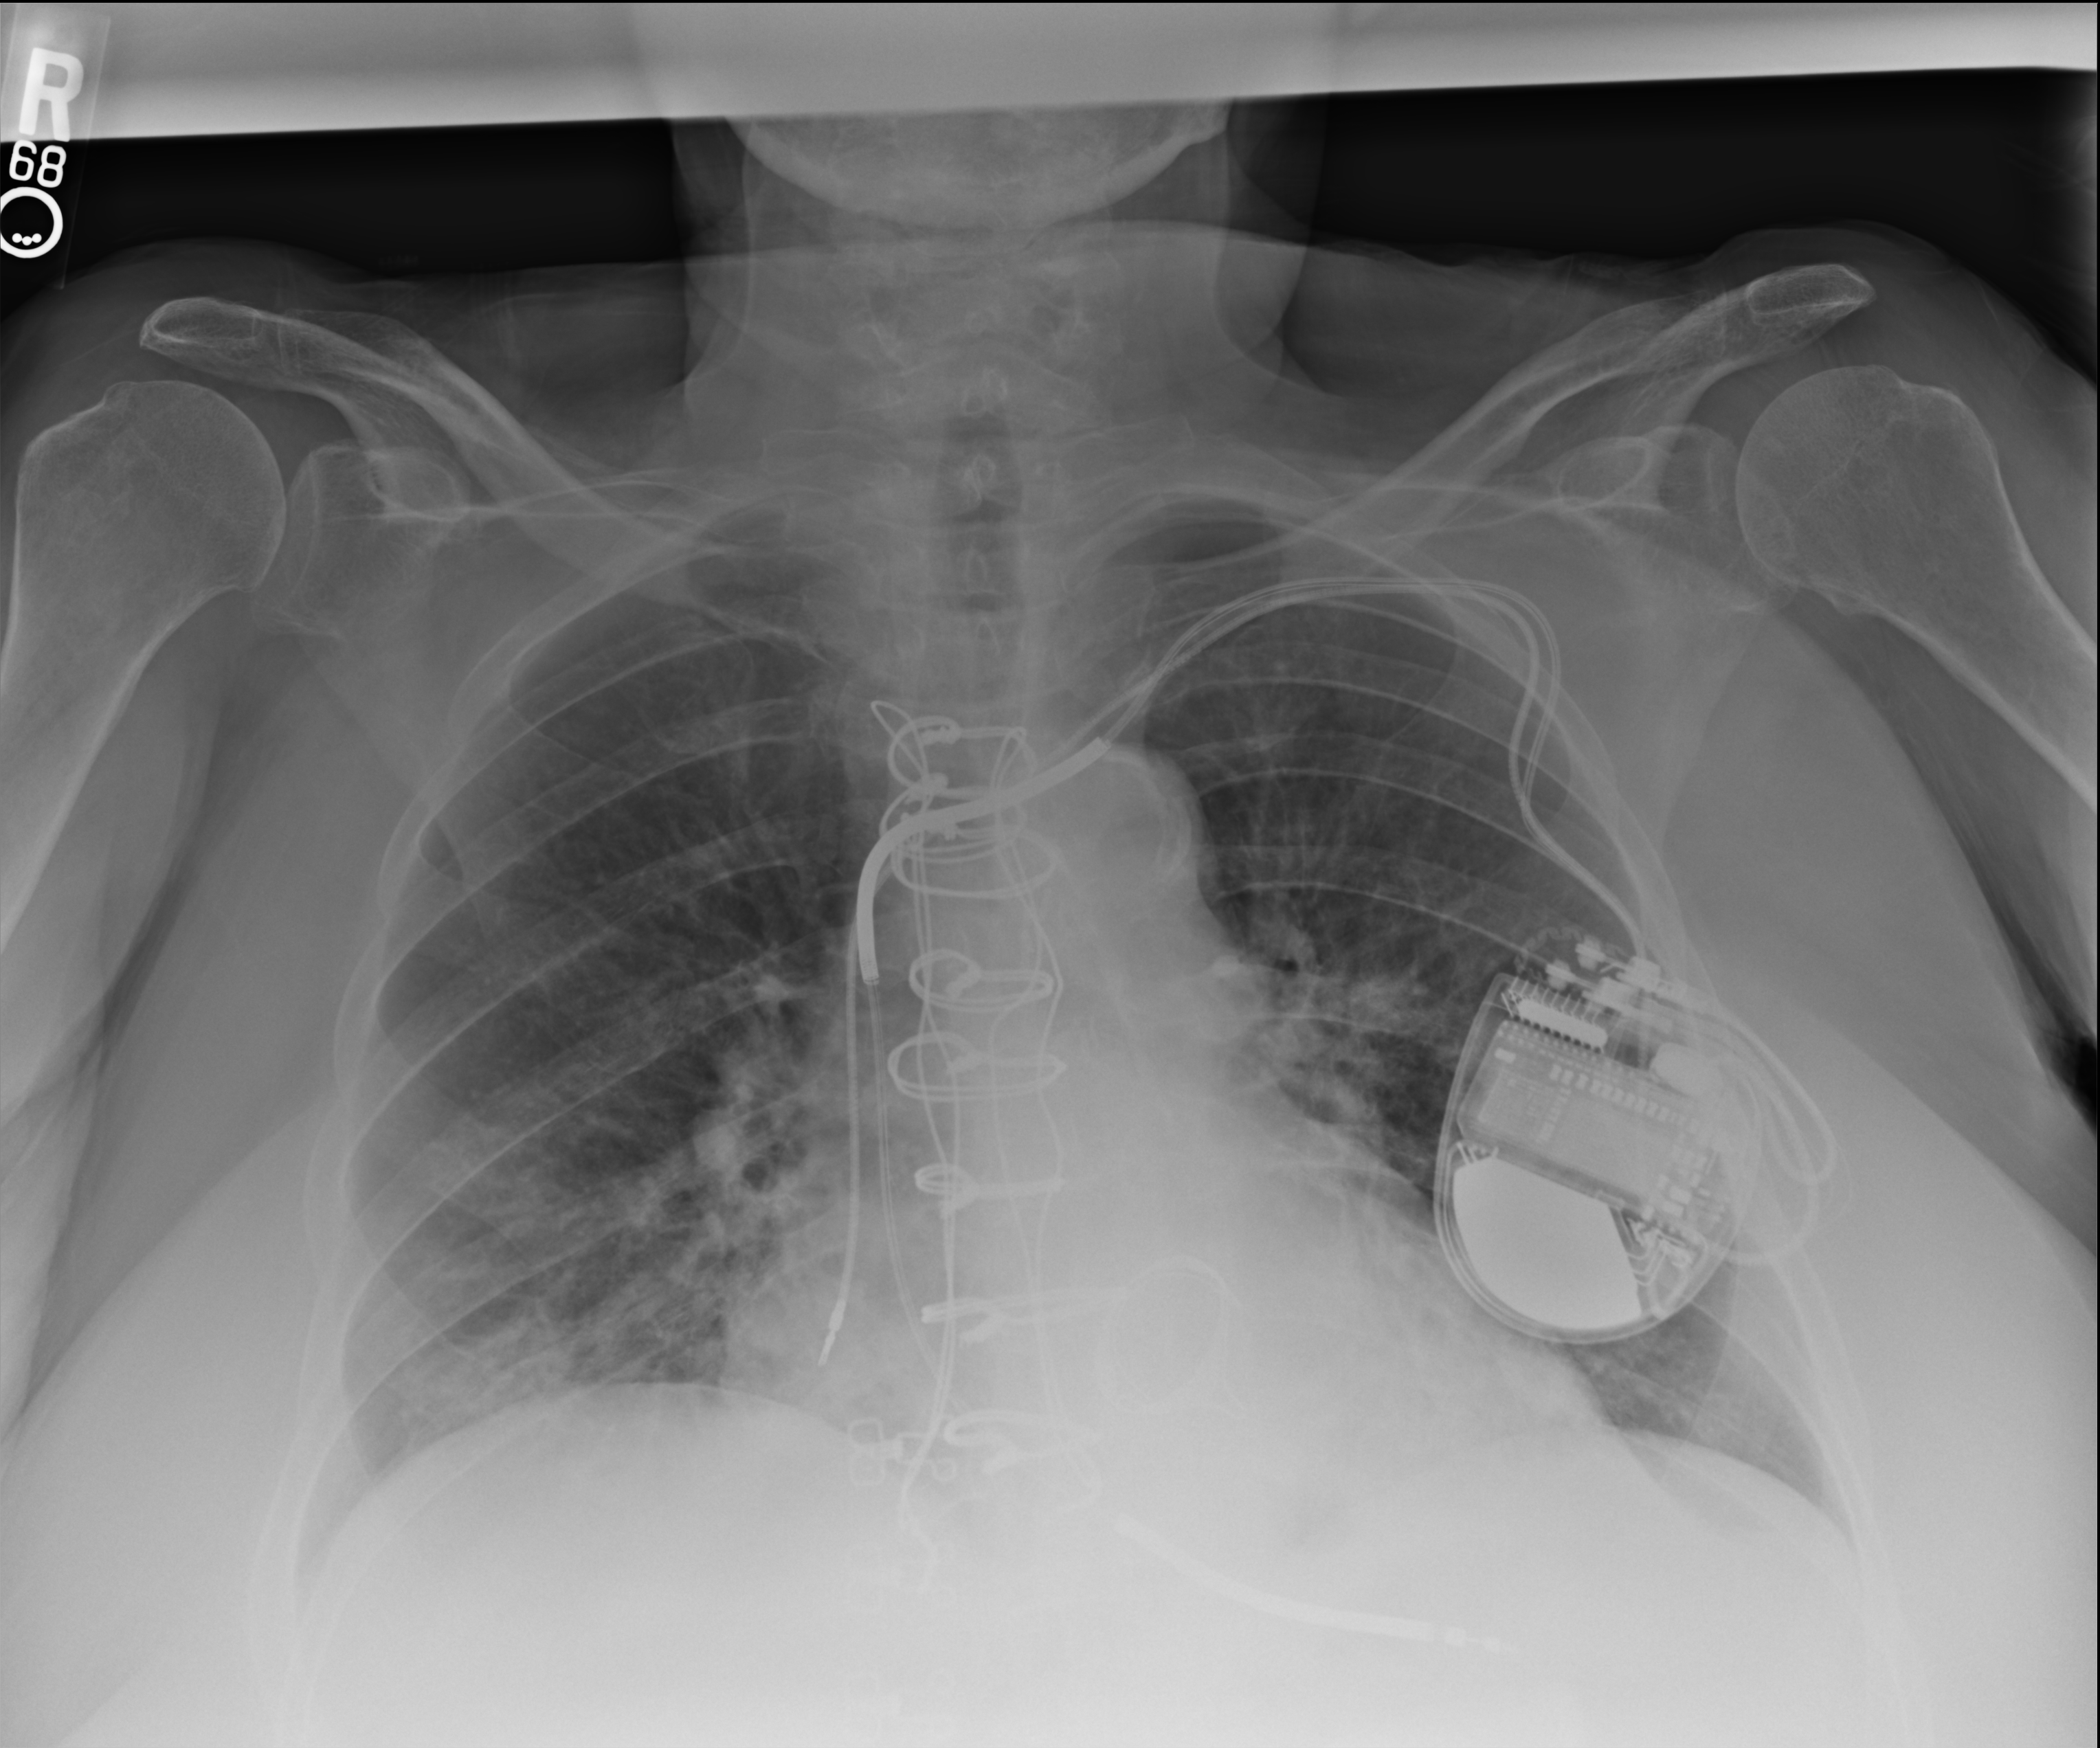
Chest radiograph; anteroposterior (AP) projection. Female patient hospitalised with COVID-19, age 60–74 years.
Admission-level facts for this patient (not findings on this image; timing relative to this image not recorded):
- admitted to intensive care during this hospital stay: yes